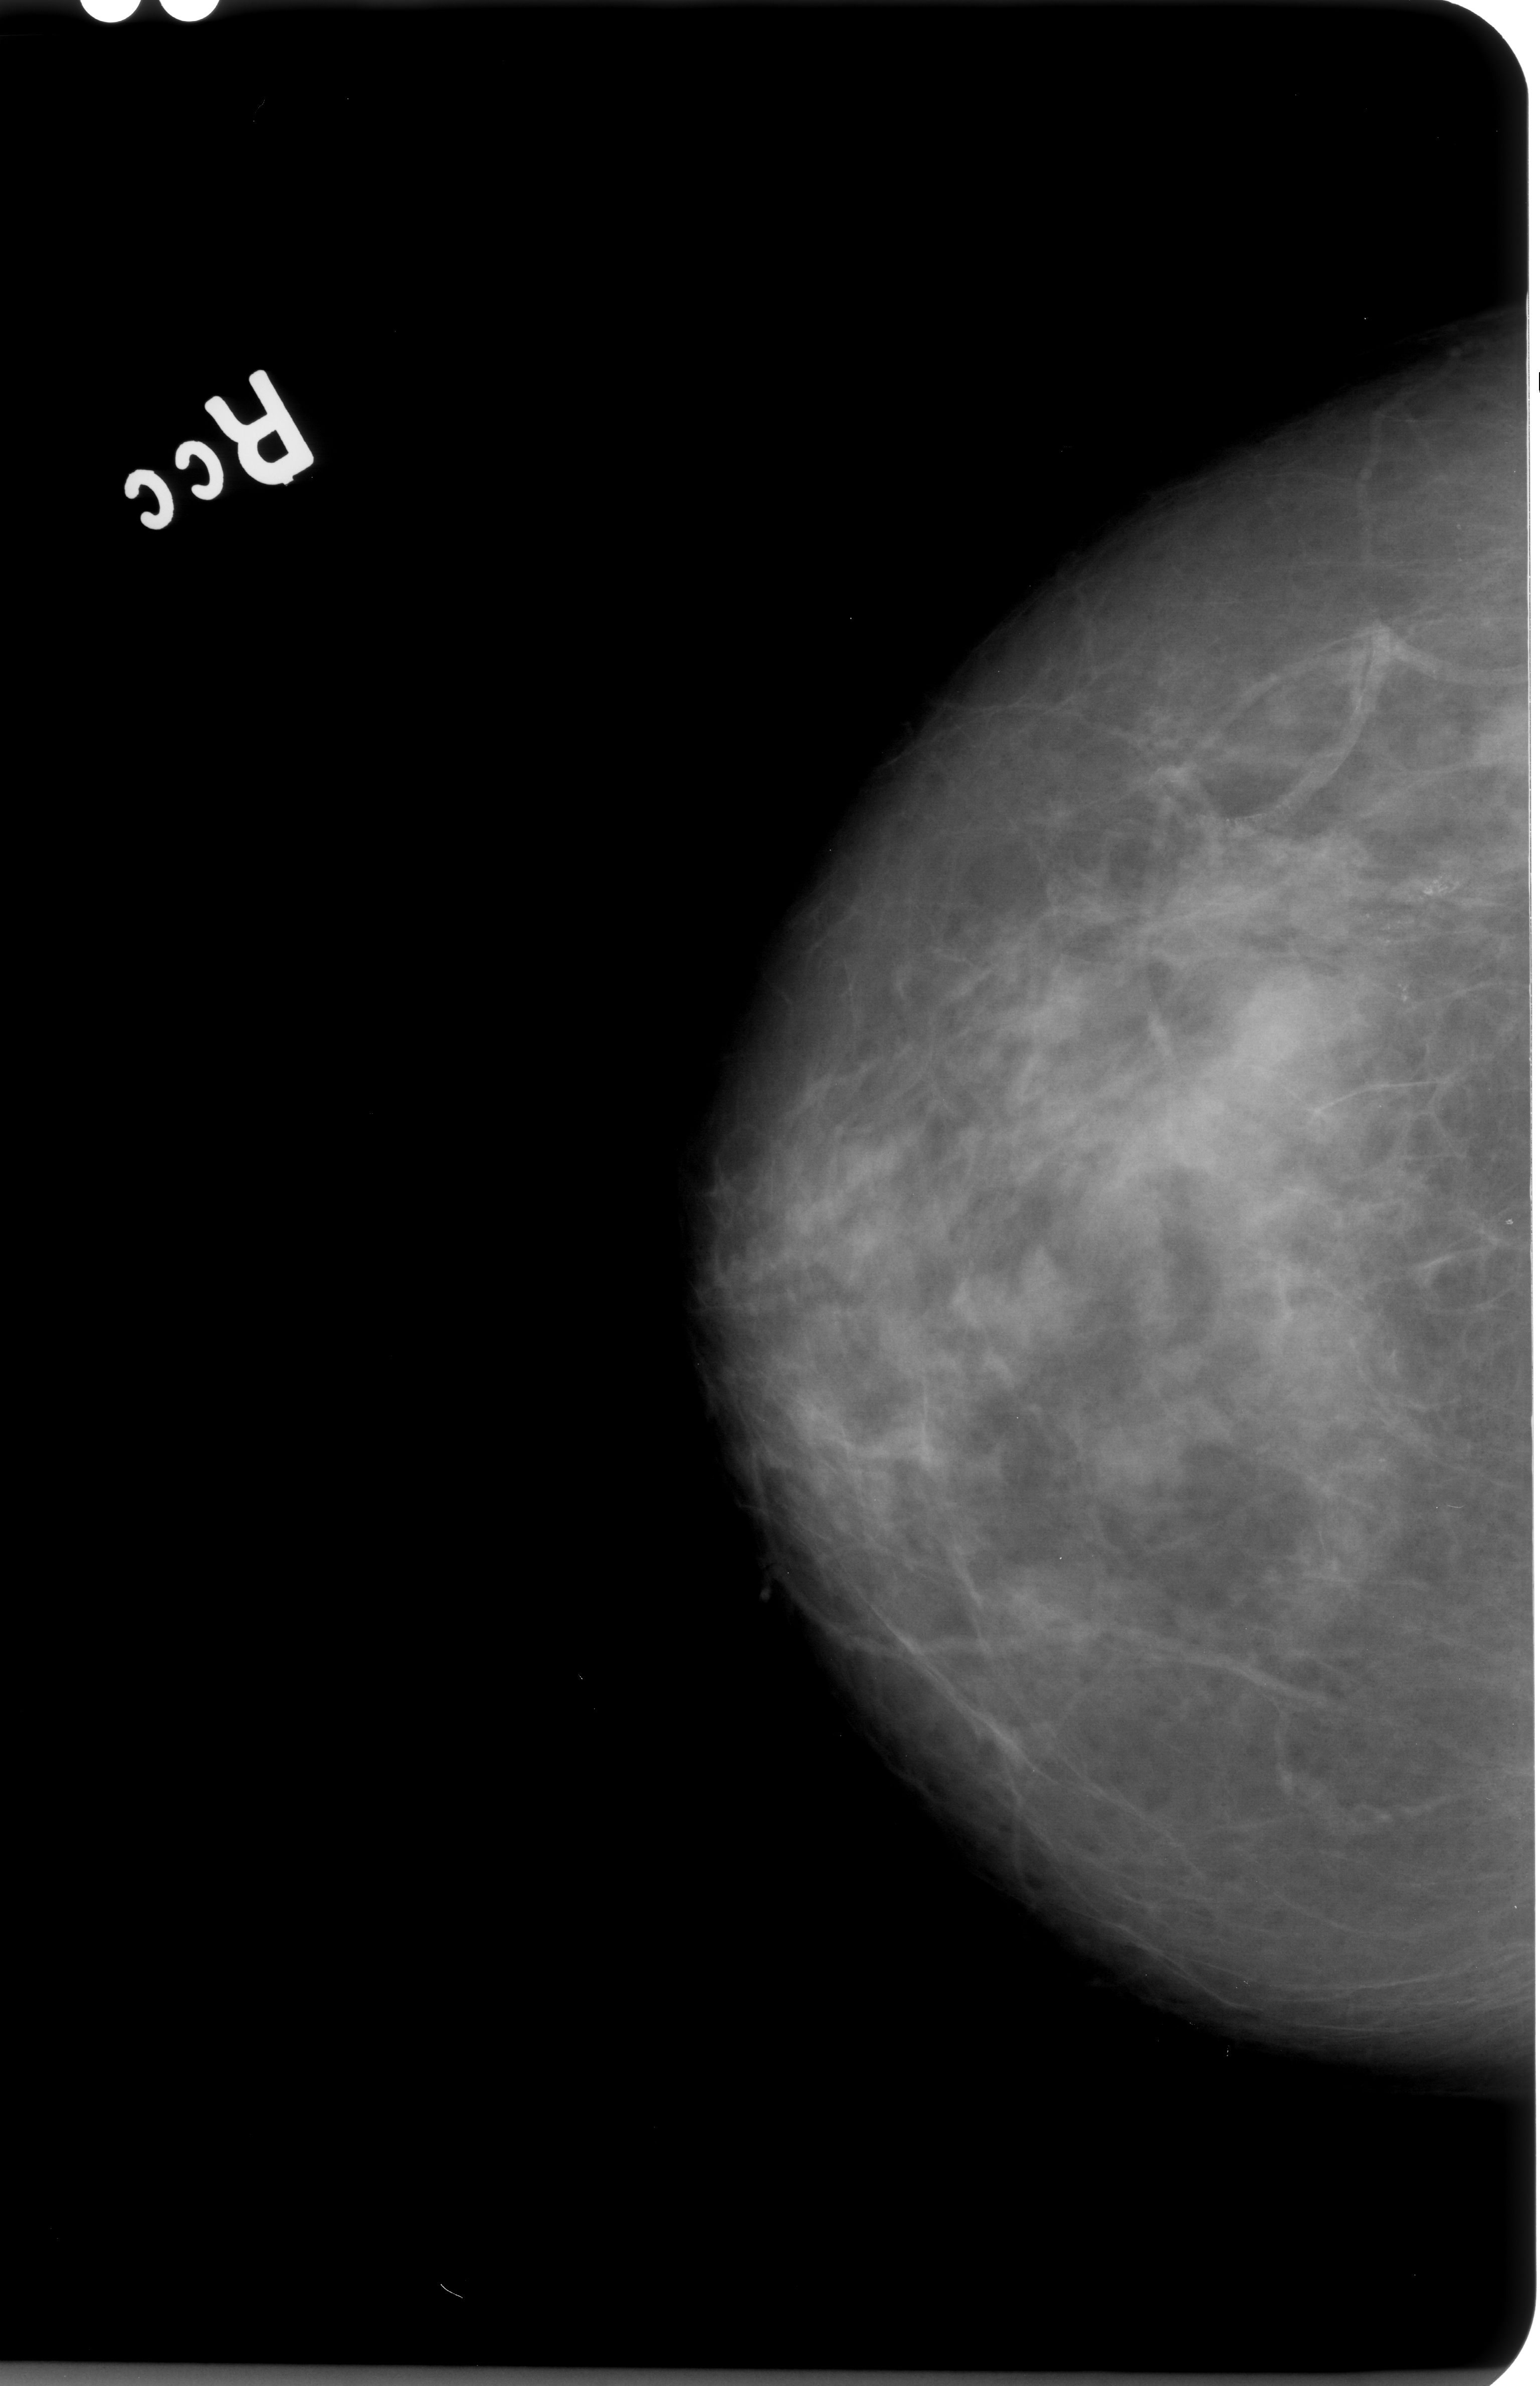
Scanned film-screen mammogram; right breast; craniocaudal (CC) view; BI-RADS breast density category 3 (scale 1–4); 1540 × 2386 image matrix.
Expert-marked regions of interest on this film, with their recorded descriptors:
- calcifications, morphology pleomorphic / fine linear branching, distribution clustered; BI-RADS assessment category 4; subtlety rating 3 on a 1 (subtle) to 5 (obvious) scale; pathology result (as recorded, not read from the image): benign: box from (x=1323, y=834) to (x=1493, y=1024) px